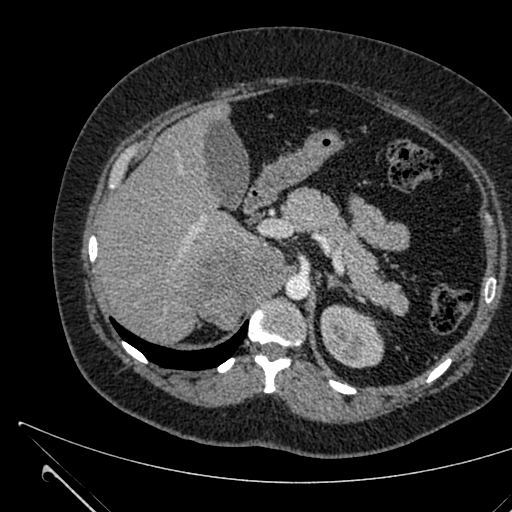
Contrast-enhanced abdominal CT, one axial slice. Position 441 of 731 along the scan axis. Intravenous contrast given. Soft-tissue window (W 400 / L 40 HU). 1 mm slice thickness. 512 × 512 image matrix, field of view 376 × 376 mm. Female patient, age 36 years. Case-level facts recorded for this patient, not image findings: diagnosis: adrenocortical carcinoma; tumour side: right adrenal; tumour size at pathology: 10 cm; Ki-67 index: 20 %; stage (as recorded): 4.
Annotated regions visible in this slice (semi-automatically segmented with operator editing):
- mass: bounding box <190,242,287,329> (left, top, right, bottom; pixels)